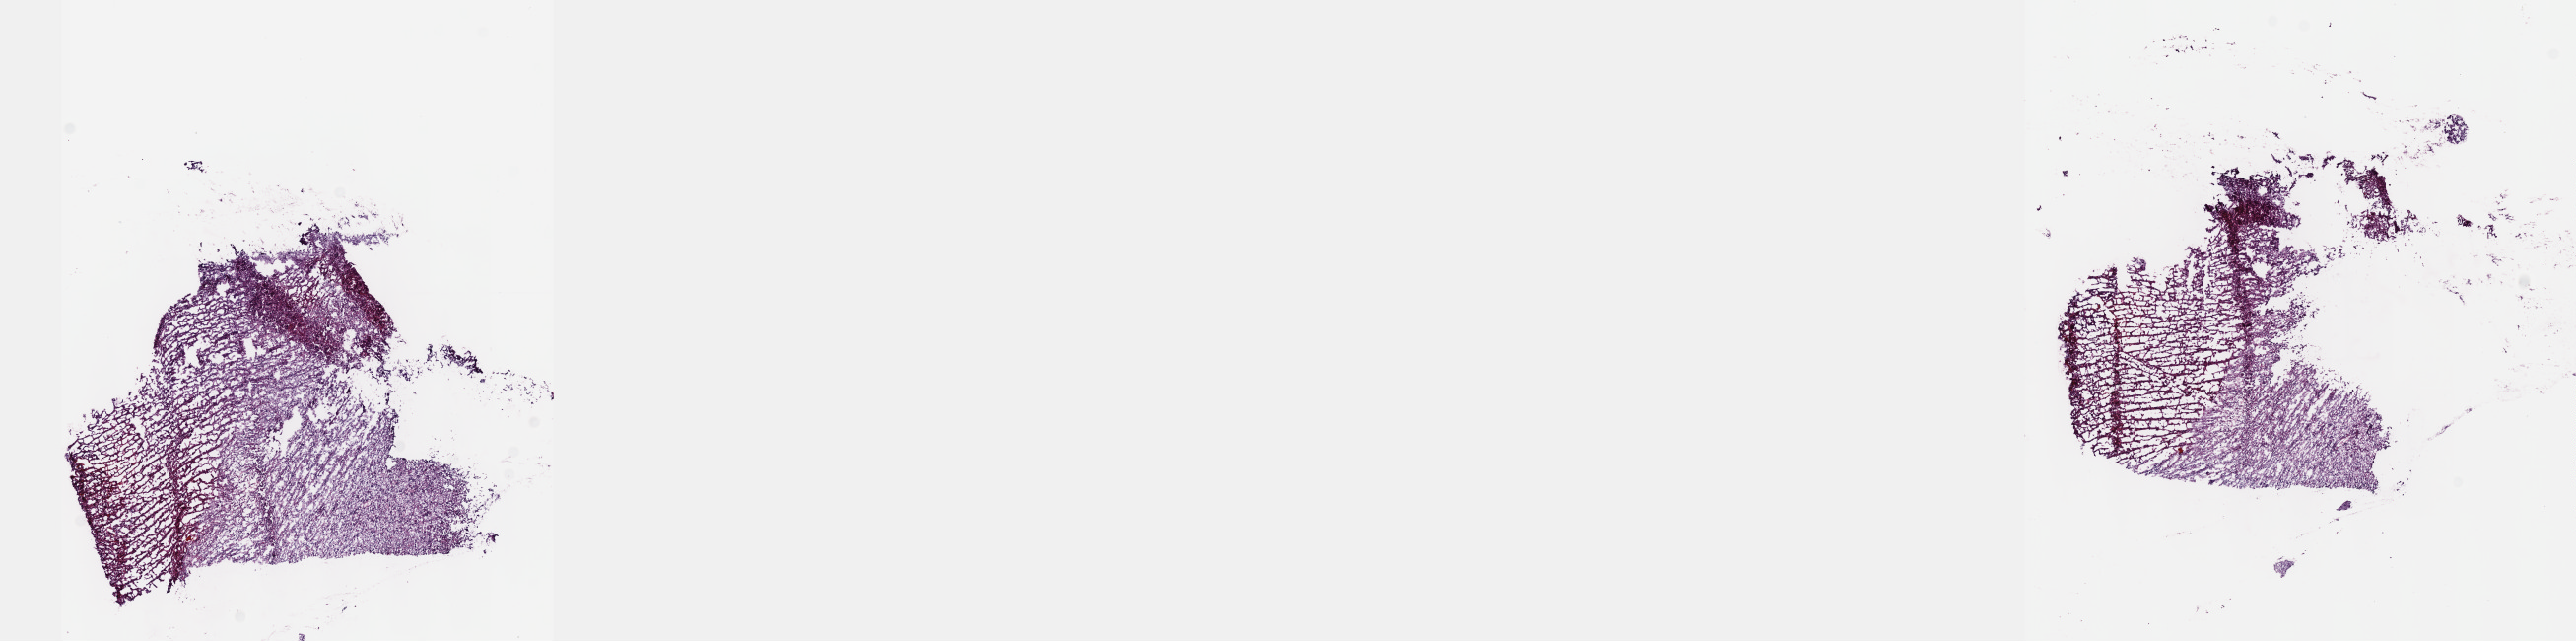
Digitized Hematoxylin and eosin (H&E) stained tissue section (whole slide), a low-resolution overview of the entire scanned area, about 21.1 x 5.3 mm. Frozen section. Recurrent tumour sample from the brain. Male, age 43 years at initial diagnosis. Composition of this section per pathologist review: tumour cells 70%, tumour nuclei 90%, normal cells 5%, stromal cells 25%, necrosis 0%. Inflammatory infiltration, as recorded: lymphocyte infiltration 0%, monocyte infiltration 0%, neutrophil infiltration 0%.
• this section: recurrent tumour
• patient diagnosis: Mixed glioma (cerebrum)